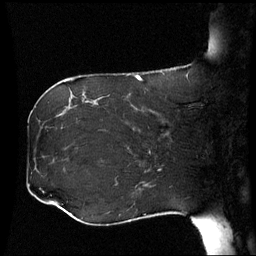
Breast MRI (dynamic contrast-enhanced), one sagittal slice. Slice 22 of 60 in the series (ordered by position). Dynamic contrast-enhanced series, image 2 of 3 at this slice position (ordered by acquisition). 1.5 T. TE 4.2 ms, TR 8.9 ms. 2.5 mm slice thickness. 256 × 256 image matrix, field of view 230 × 230 mm. Patient: female, 42 years. From the clinical record (not read from this slice): setting: breast cancer imaged before/during neoadjuvant chemotherapy; receptor status: HER2-positive.
Outlined on this slice (semi-automatic segmentation, software-assisted and operator-edited):
- analysis volume of interest (the breast-tissue region the enhancement analysis was run in; not a lesion): bounding box (x1, y1, x2, y2) in pixels: (106, 102, 173, 150)
- tumour enhancement mask (voxels above the 70 % enhancement threshold inside the analysis volume of interest): (151, 111, 158, 114)